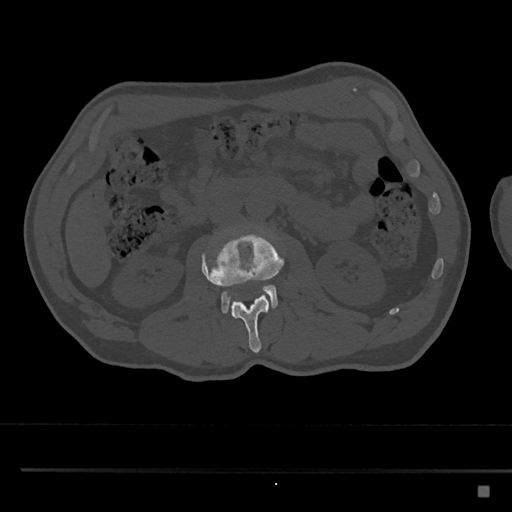
CT including the spine, one axial slice; position 738 of 797 along the scan axis; 120 kVp; bone window (W 1800 / L 400 HU); 0.5 mm slice thickness; 512 × 512 image matrix, field of view 391 × 391 mm. Male patient, age 59 years. Case-level facts recorded for this patient, not image findings: primary cancer: prostate.
Annotated regions visible in this slice (semi-automatically segmented with operator editing):
- L2 vertebra: bounding box (x1, y1, x2, y2) in pixels: (201, 230, 284, 353)
- L3 vertebra: (221, 284, 279, 314)